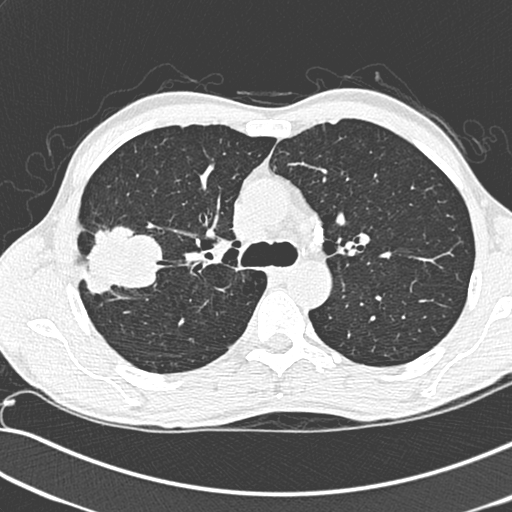
Low-dose screening chest CT, one axial slice; slice 201 of 281 in the series (ordered by position); 120 kVp; lung window (W 1500 / L -600 HU); 1.3 mm slice thickness; 512 × 512 image matrix, field of view 341 × 341 mm.
Outlined on this slice (expert manual segmentation):
- lesion 1 (tumor, upper lobe of right lung): bounding box (x1, y1, x2, y2) in pixels: (75, 224, 165, 301)